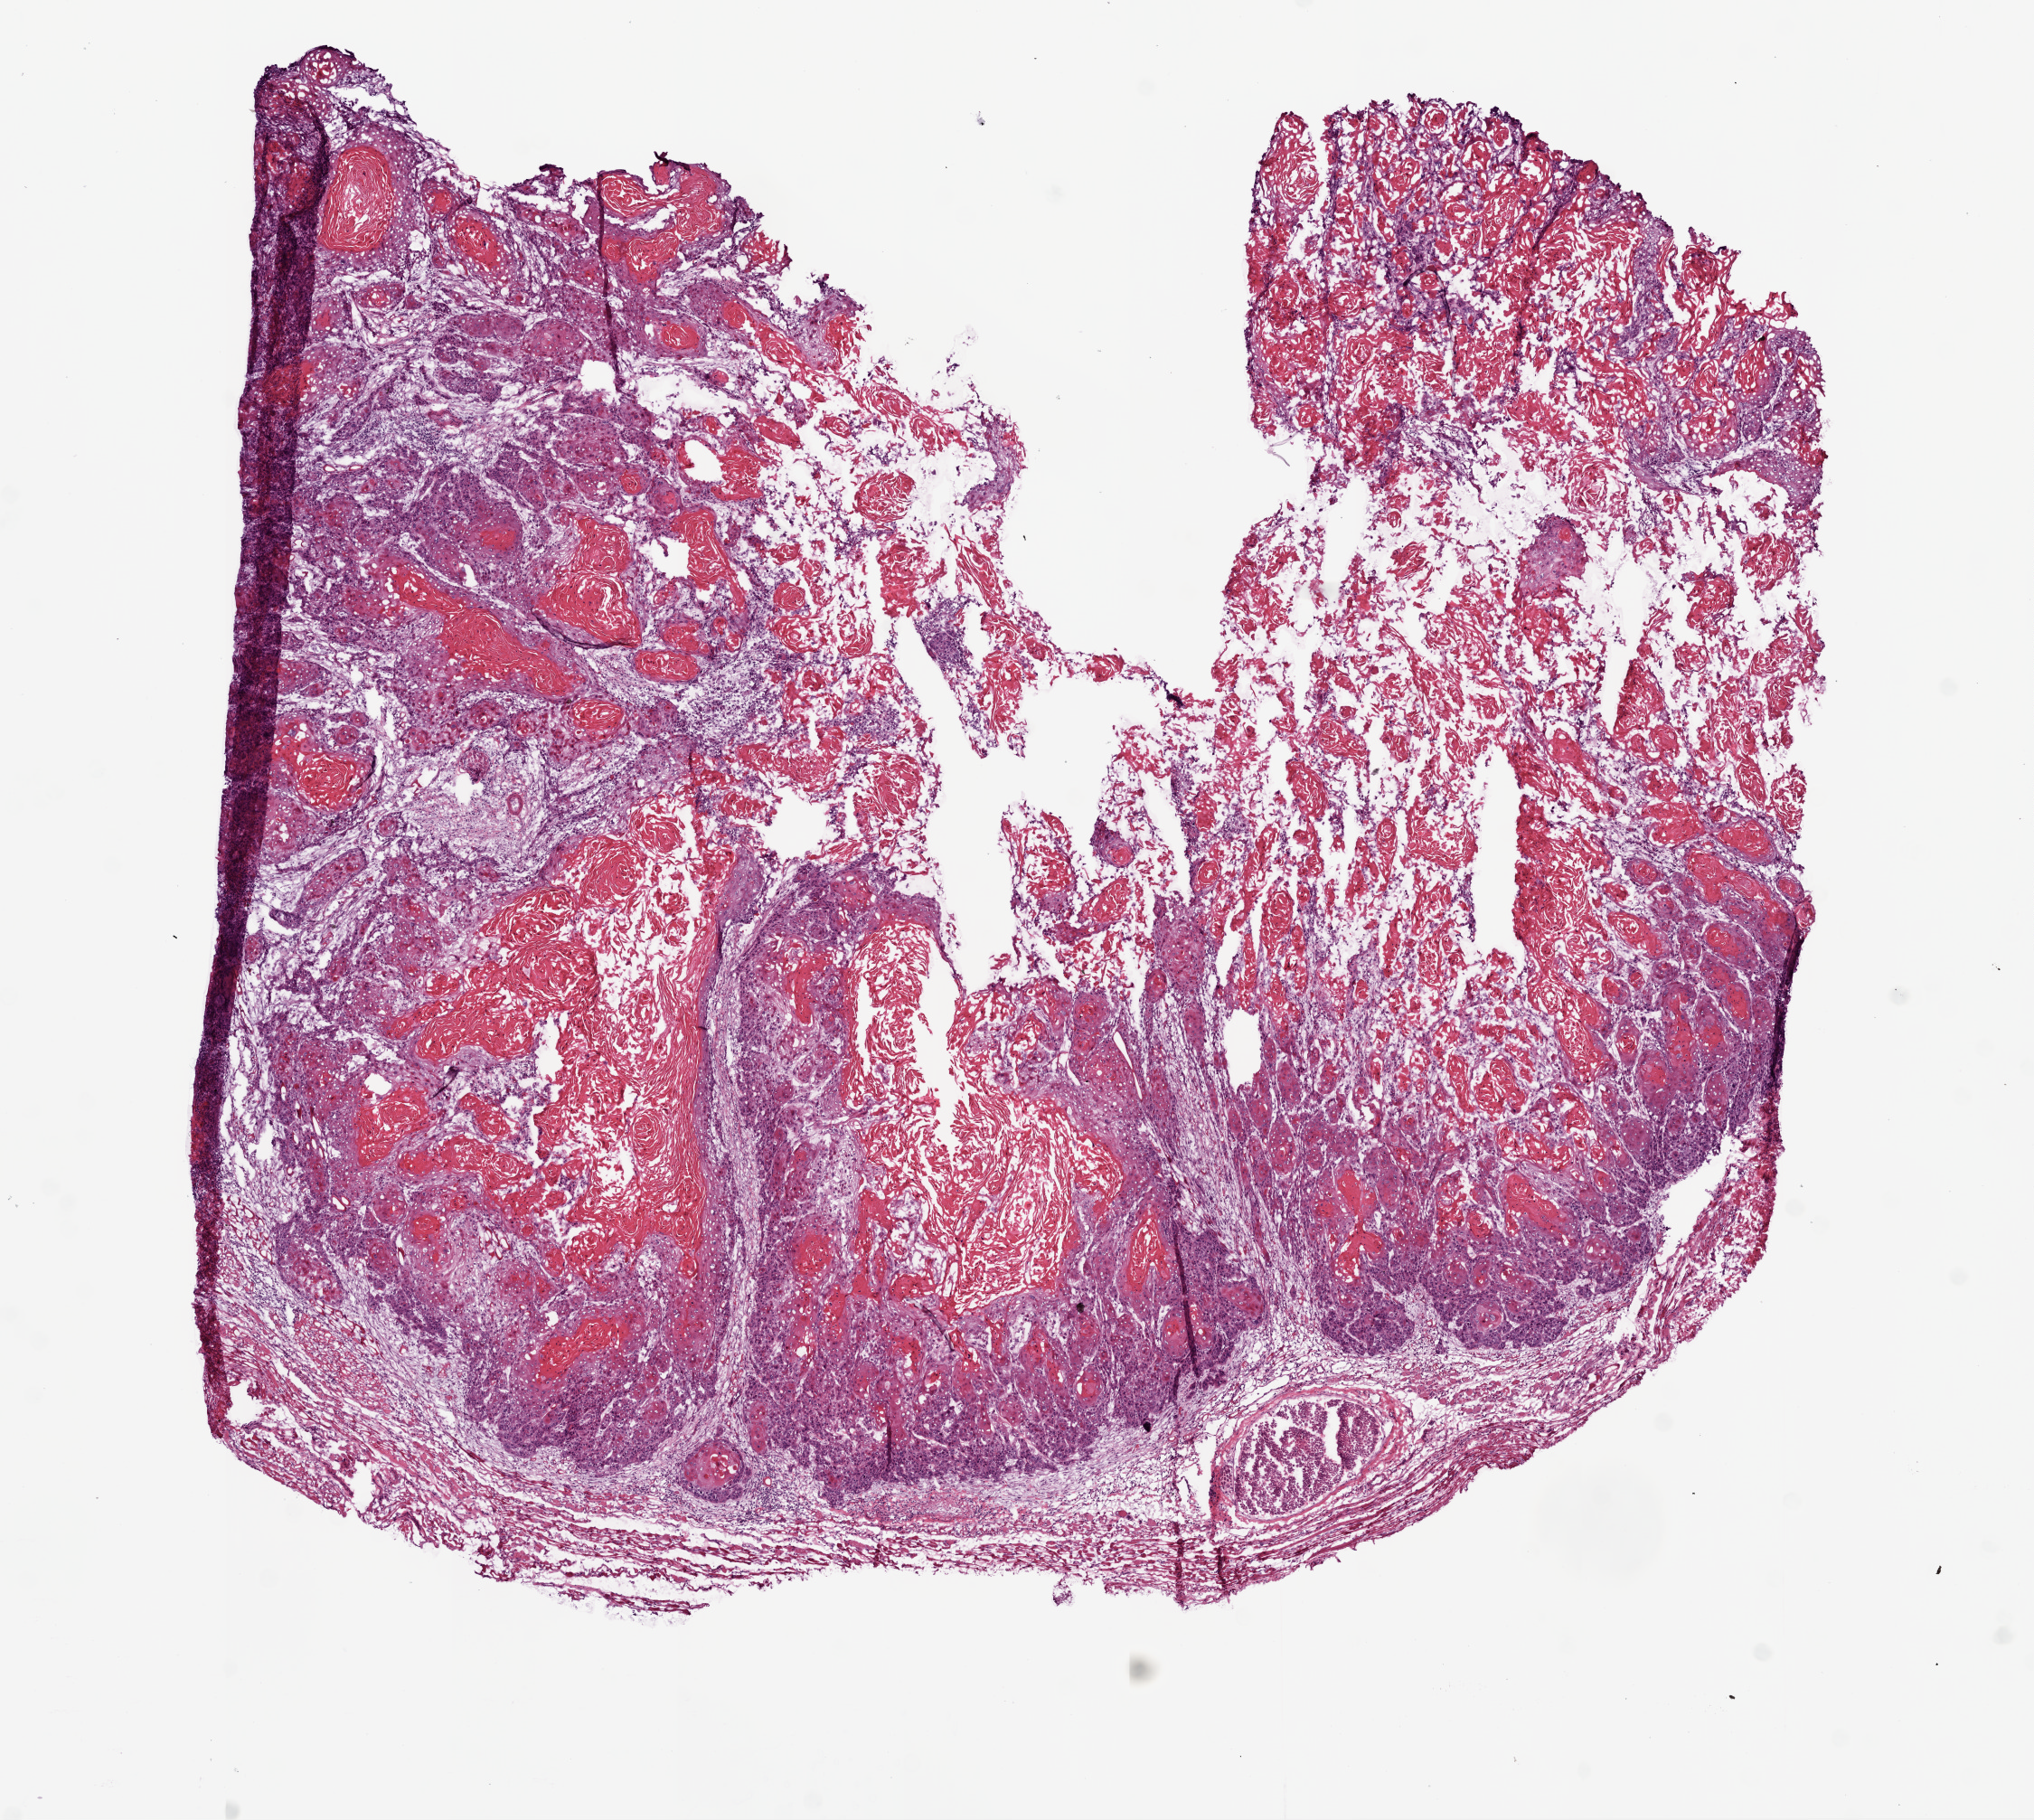
Digitized Hematoxylin and eosin (H&E) stained tissue section (whole slide), a low-resolution overview of the entire scanned area, about 9.0 x 8.1 mm, frozen section from the bottom of the tissue portion, sample: primary tumour, head and neck. Male, age 19 years at initial diagnosis. Histologic grade: G2 (moderately differentiated). Pathologist review of this section (percent, as recorded): tumour cells 85%, tumour nuclei 85%, normal cells 0%, stromal cells 15%, necrosis 0%.
* AJCC pathologic stage: IVA (7th edition)
* histologic diagnosis: Squamous cell carcinoma, NOS